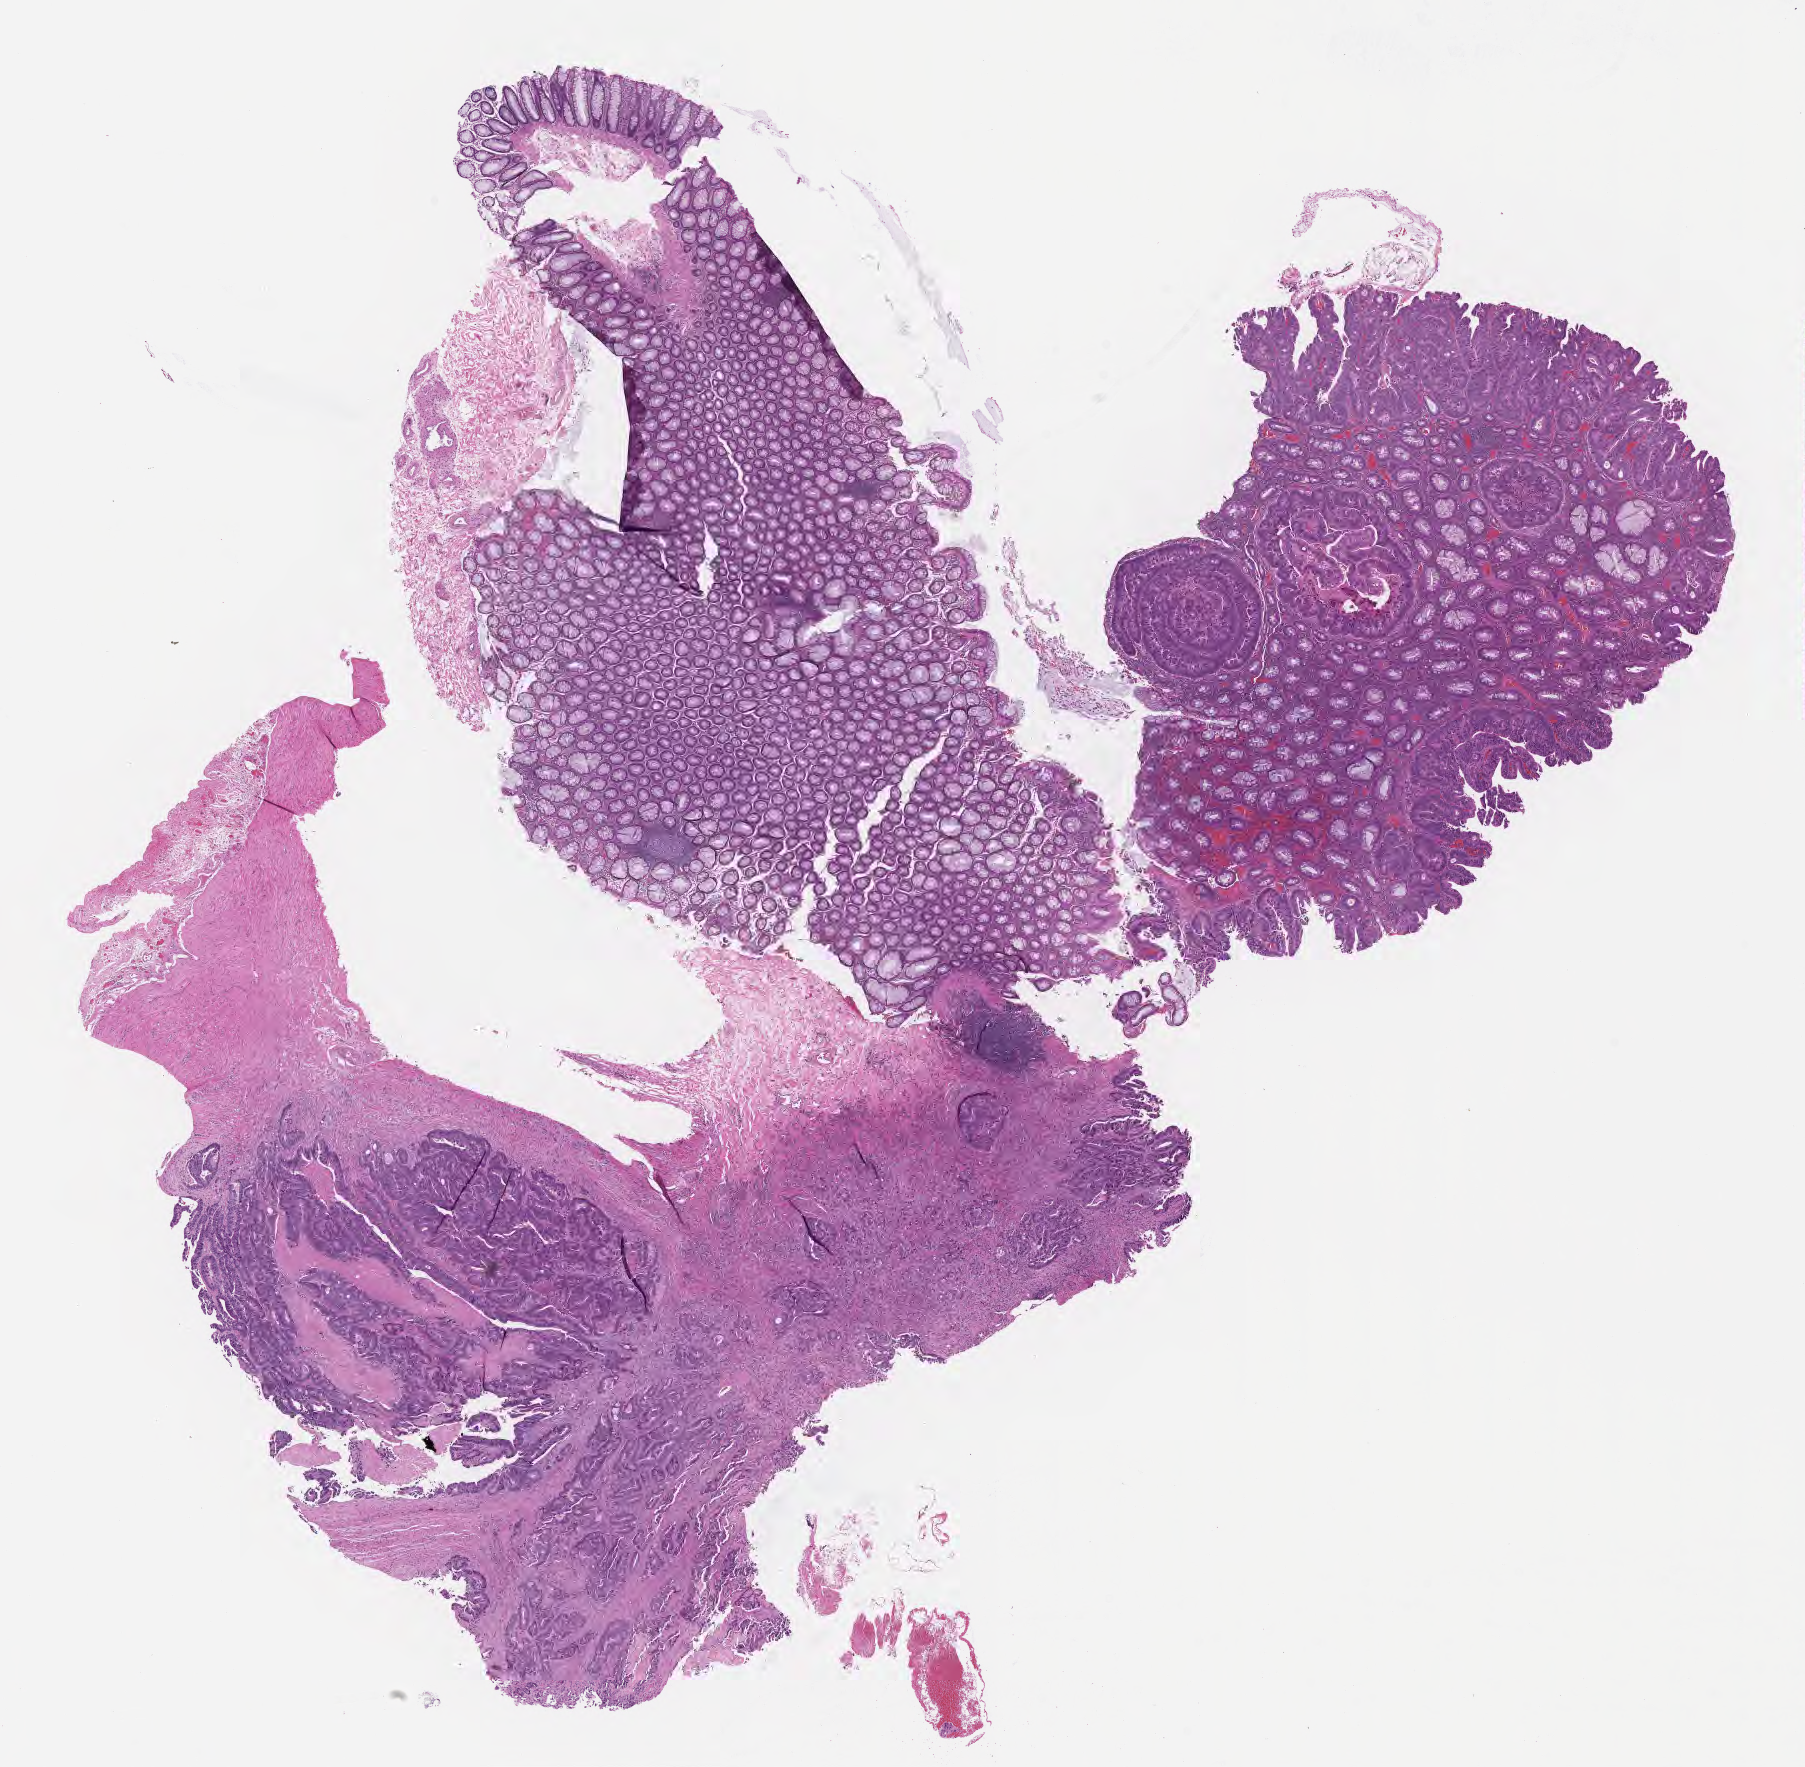
Haematoxylin and eosin whole-slide image, a low-resolution overview of the entire scanned area, about 14.6 x 14.3 mm; FFPE section; primary tumor; site: sigmoid colon. Male, age 72 years at initial diagnosis. Tumor grade: G2 (moderately differentiated). Composition of this section per pathologist review: tumor cells 50%, tumor nuclei 55%, stromal cells 0%, necrosis 0%, normal cells 50%. Inflammatory infiltration, as recorded: lymphocyte infiltration 0%, monocyte infiltration 0%, neutrophil infiltration 0%.
AJCC pathologic stage: Stage IIA. Histologic diagnosis: Adenocarcinoma, NOS.